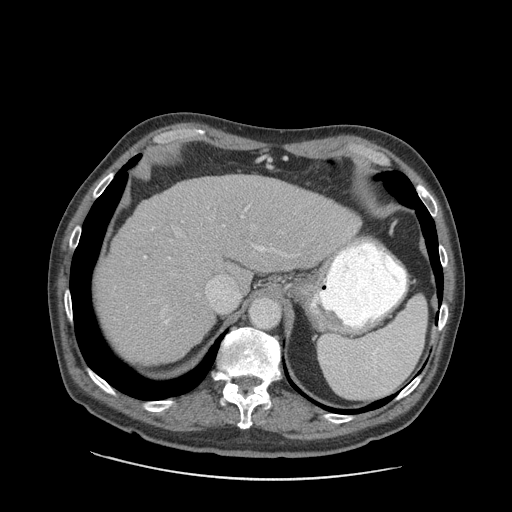
Contrast-enhanced abdominal CT (liver protocol), one axial slice; reconstruction kernel STANDARD; soft-tissue window (W 400 / L 40 HU); 2.5 mm slice thickness; 512 × 512 image matrix, field of view 420 × 420 mm. From the clinical record (not read from this slice): diagnosis: hepatocellular carcinoma (patient treated with transarterial chemoembolisation; whether this scan precedes or follows treatment is not stated here); TNM stage (as recorded): Stage-I; Child-Pugh class: A.
Structures marked on this image (semi-automatic segmentation, software-assisted and operator-edited):
- liver parenchyma outside the tumour (the mass and vessels are separate outlines, so this box may not span the whole liver): bounding box <98,174,360,364> (left, top, right, bottom; pixels)
- liver vessels: <144,203,351,323>